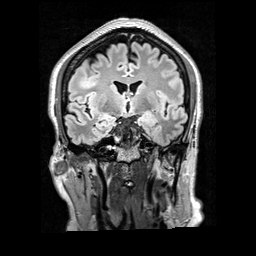
Brain MRI from a brain-tumour surgery series, one coronal slice. Slice 108 of 200 in the series (ordered by position). T2 FLAIR. 256 × 256 image matrix. From the clinical record (not read from this slice): histopathology: Glioblastoma; WHO grade: 4; IDH mutation: no.
Structures marked on this image (manually delineated by an expert):
- tumour: bounding box <79,71,100,89> (left, top, right, bottom; pixels)